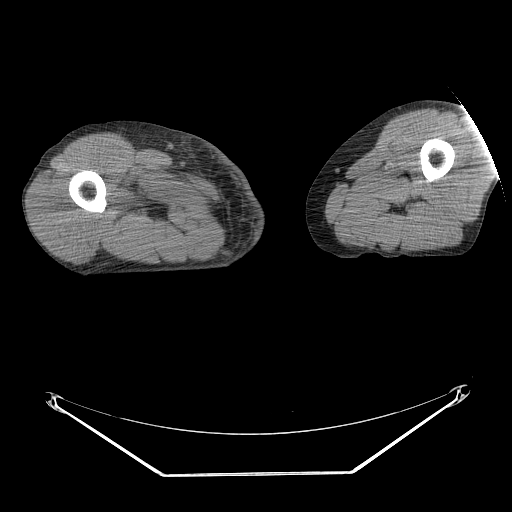
CT of an extremity soft-tissue mass (from a PET/CT study), one axial slice. Position 232 of 311 along the scan axis. Reconstruction kernel STANDARD. Soft-tissue window (W 400 / L 40 HU). 3.75 mm slice thickness. 512 × 512 image matrix, field of view 500 × 500 mm. Male patient. Case-level facts recorded for this patient, not image findings: histological type: undifferentiated - pleiomorphic; grade: high; site of the primary tumour: right thigh.
Outlined on this slice (expert contour drawn on MRI and transferred to this co-registered scan by the dataset authors):
- gross tumour volume including surrounding oedema: bounding box (x1, y1, x2, y2) in pixels: (141, 194, 159, 215)